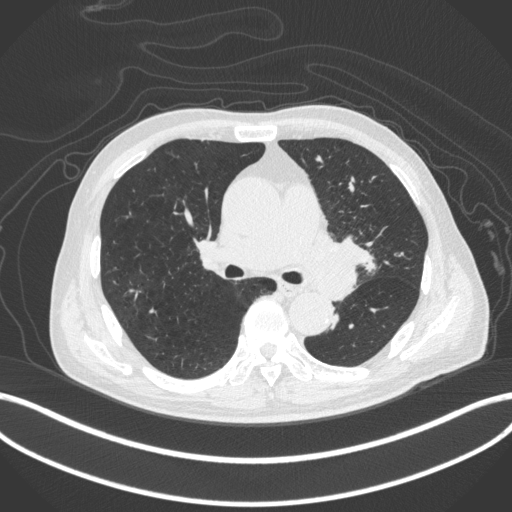
Chest CT, one axial slice. Position 258 of 420 along the scan axis. Reconstruction kernel B31f. Lung window (W 1500 / L -600 HU). 1 mm slice thickness. 512 × 512 image matrix, field of view 400 × 400 mm. Patient: male, 77 years. Case-level facts recorded for this patient, not image findings: clinical TNM (as recorded): T3 N1 M0.
Structures marked on this image (rectangle marked by the reading radiologist):
- lung tumour (recorded histology: adenocarcinoma): box from (x=310, y=230) to (x=372, y=302) px